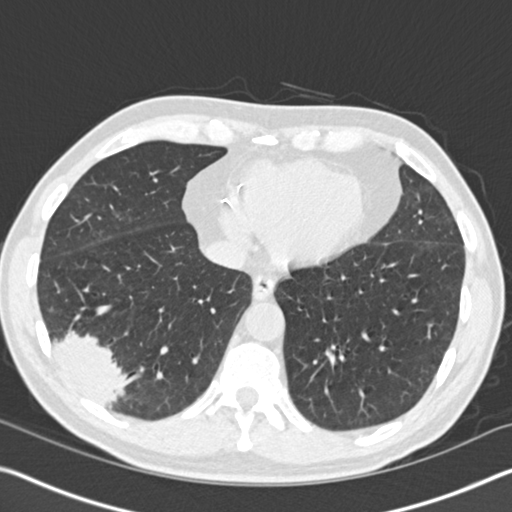
Axial slice from a low-dose chest CT screening exam. Baseline annual screen. Lung window (W 1500 / L -600 HU). 2 mm slice thickness. Slice 112 of 161 in the series. Male participant, aged 61 years at enrolment. Current smoker at enrolment.
Expert-annotated lung lesion, box from (x=26, y=296) to (x=146, y=418) px. Screening reader's record for this exam (one nodule recorded; not confirmed to be the boxed lesion): non-calcified nodule or mass ≥4 mm, right lower lobe, 52 × 36 mm, spiculated (stellate) margins, soft tissue attenuation. Official screen result: positive, change unspecified: nodule(s) >= 4 mm or enlarging nodule(s), mass(es), or other non-specific abnormalities suspicious for lung cancer.